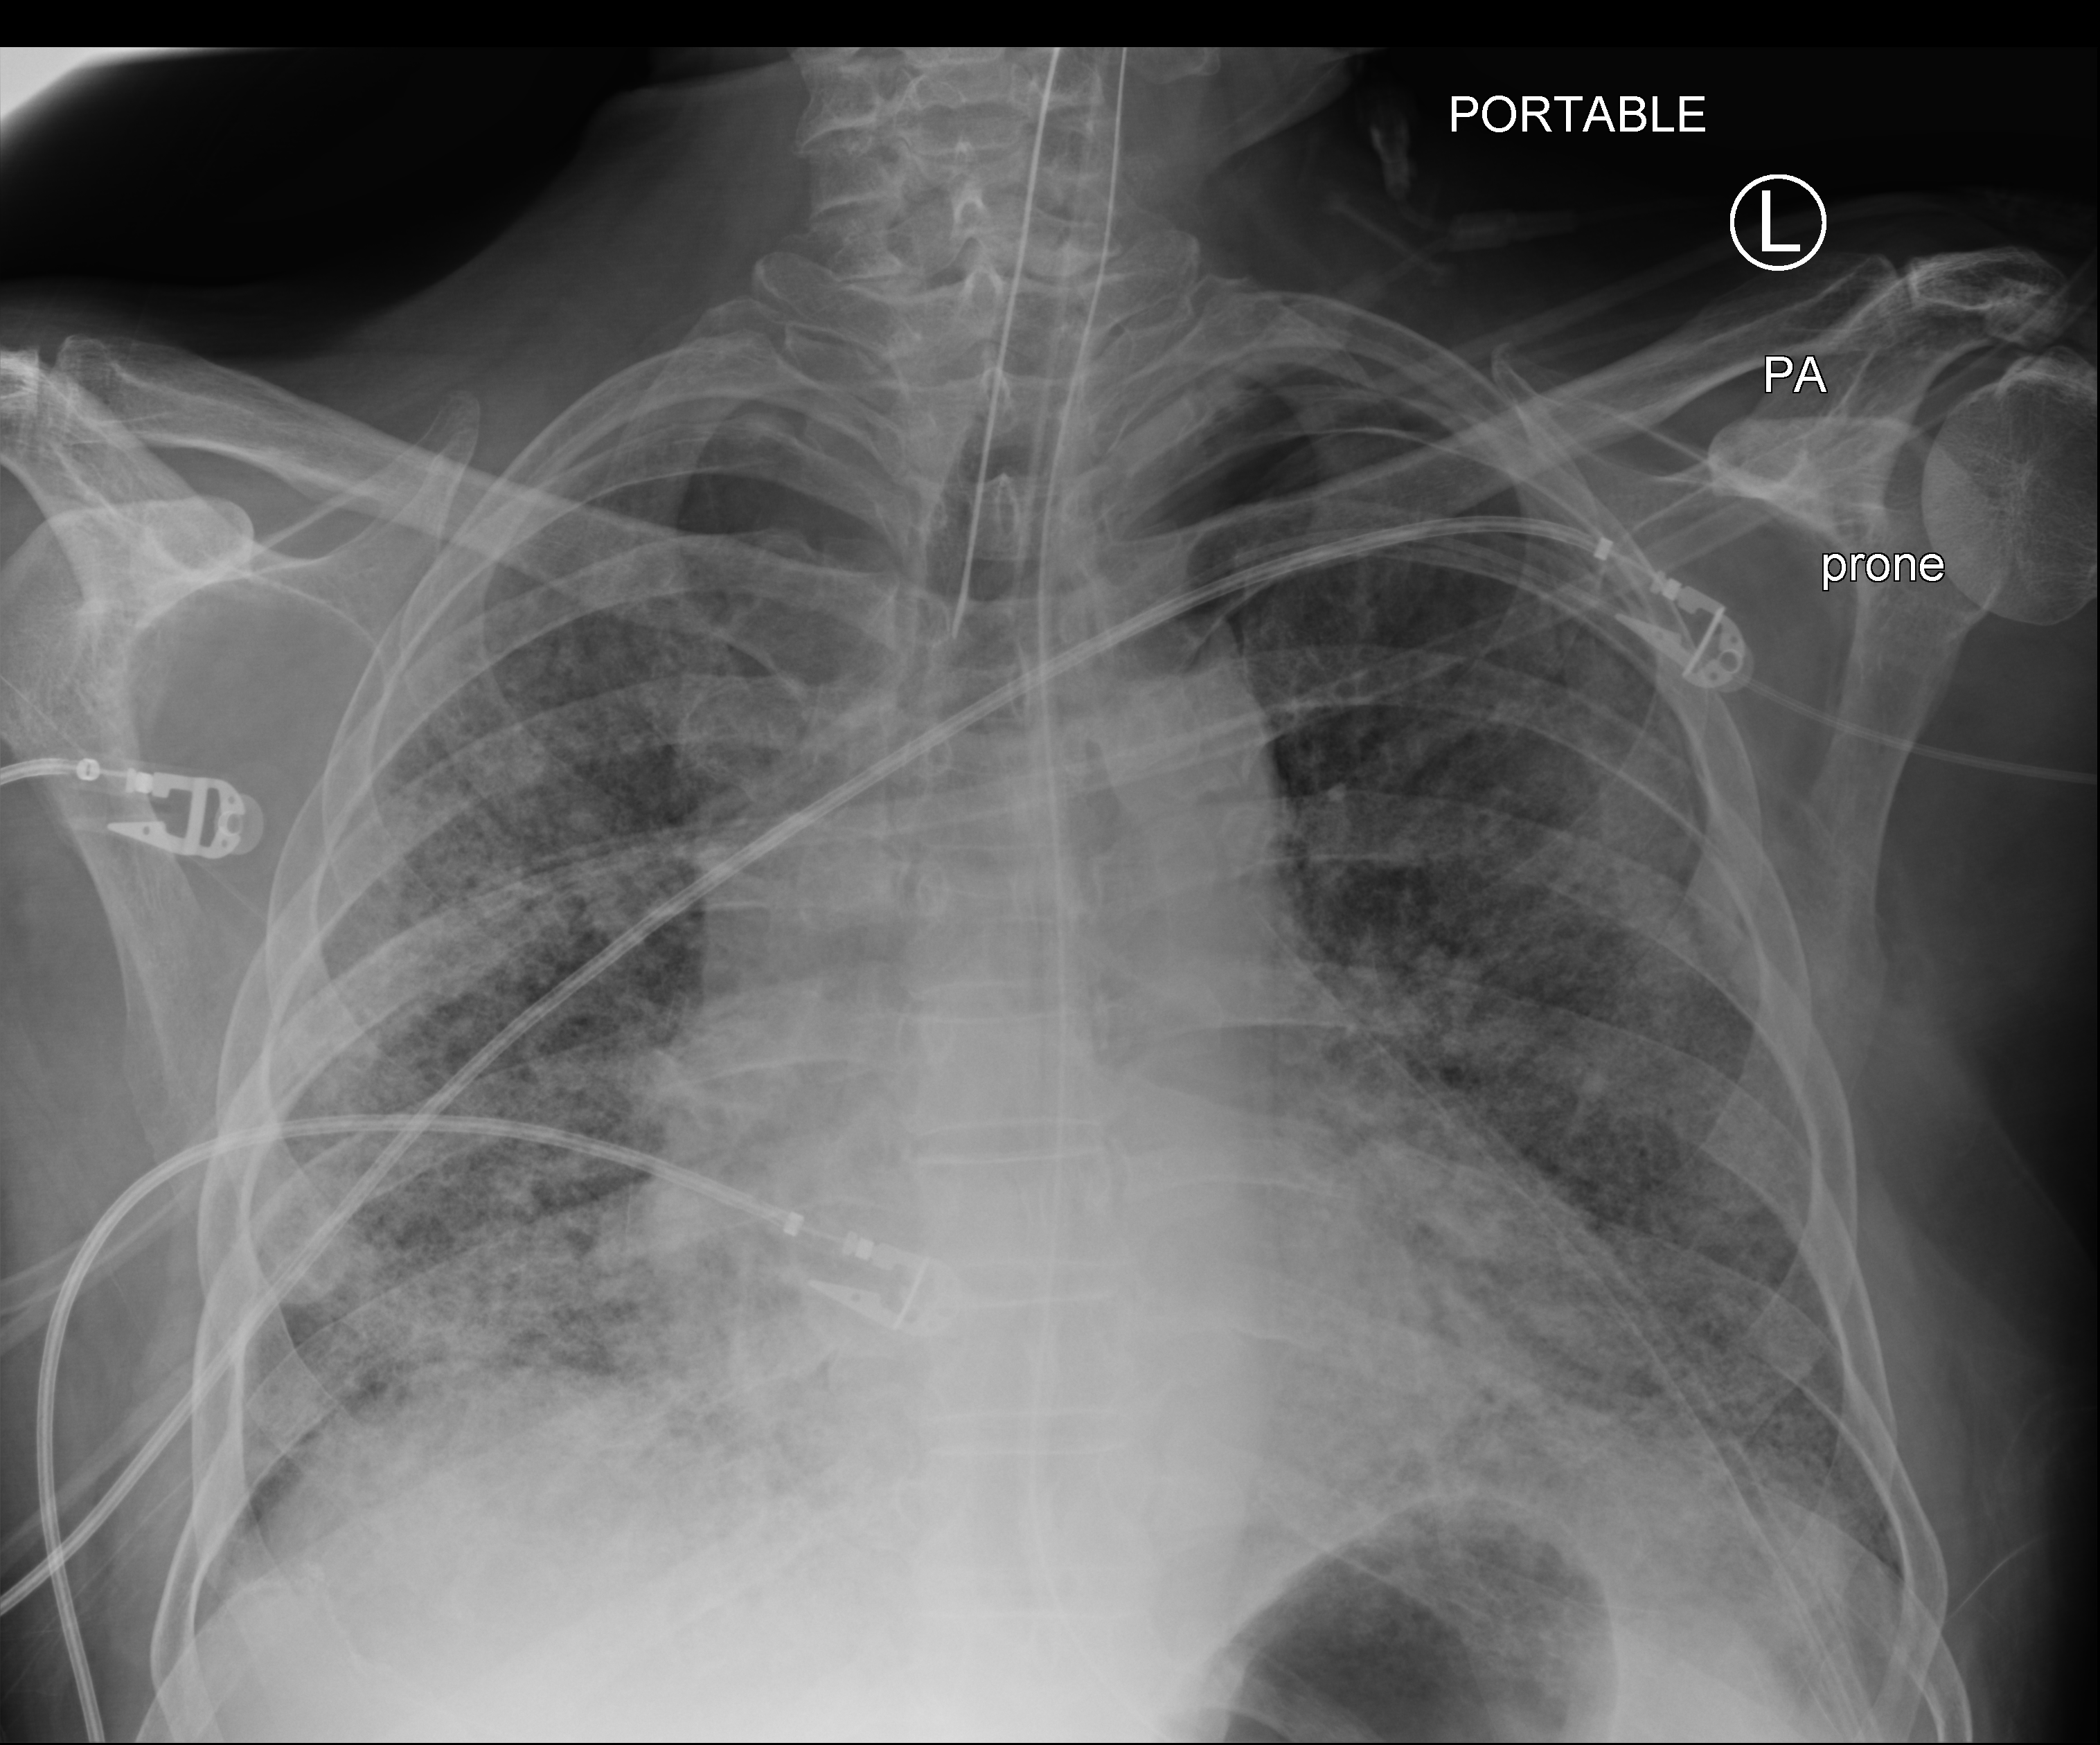
Portable chest radiograph; posteroanterior (PA) projection. Patient hospitalised with COVID-19; male, aged 60–74 years.
Hospital-stay facts (about this admission, not read from this image; timing relative to this image not recorded):
- admitted to intensive care during this hospital stay: yes
- length of hospital stay: 54 days